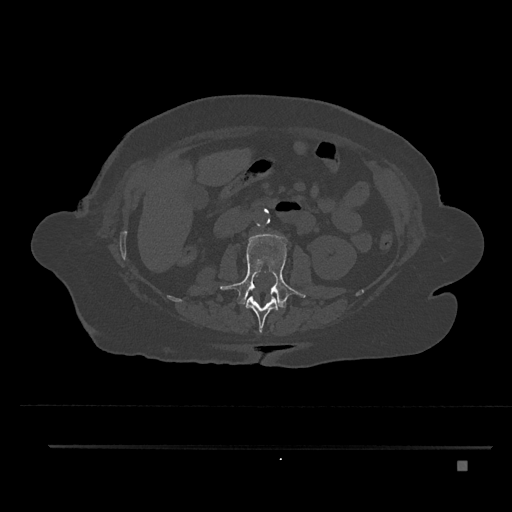
CT including the spine, one axial slice. Position 185 of 797 along the scan axis. Reconstruction kernel Br40s/3. 120 kVp. Bone window (W 1800 / L 400 HU). 512 × 512 image matrix, field of view 437 × 437 mm. Patient: female, 76 years. From the clinical record (not read from this slice): primary cancer: lung; vertebrae with lytic lesions (as recorded): T11, L3.
Annotated regions visible in this slice (semi-automatically segmented with operator editing):
- L1 vertebra: bounding box [x1, y1, x2, y2] px = [246, 295, 279, 332]
- L2 vertebra: [220, 234, 305, 309]